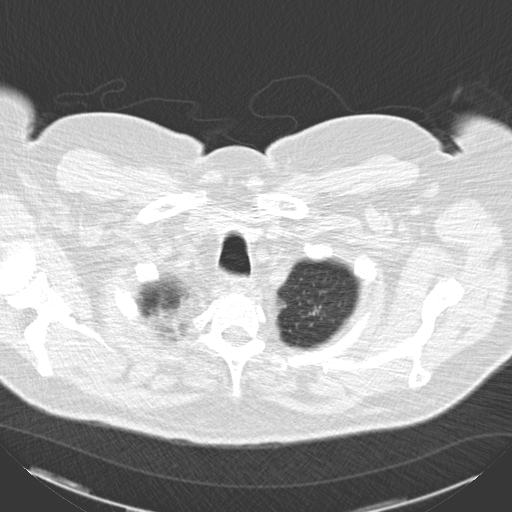
Low-dose screening chest CT, axial slice; baseline annual screen; lung window (W 1500 / L -600 HU); 5 mm slice thickness; slice 7 of 71 in the series; 512 × 512 image matrix, field of view 366 × 366 mm. Male, age 67 years at enrolment.
- Expert reader's lesion annotation, bounding box [x1, y1, x2, y2] px = [298, 299, 332, 325].
- No non-calcified nodule or mass ≥4 mm was recorded by the screening reader at this exam.
- Lung cancer was diagnosed 891 days after this screen: adenocarcinoma, NOS, left upper lobe, moderately differentiated (G2), stage IIA (AJCC 6th edition), 18 mm at pathology.